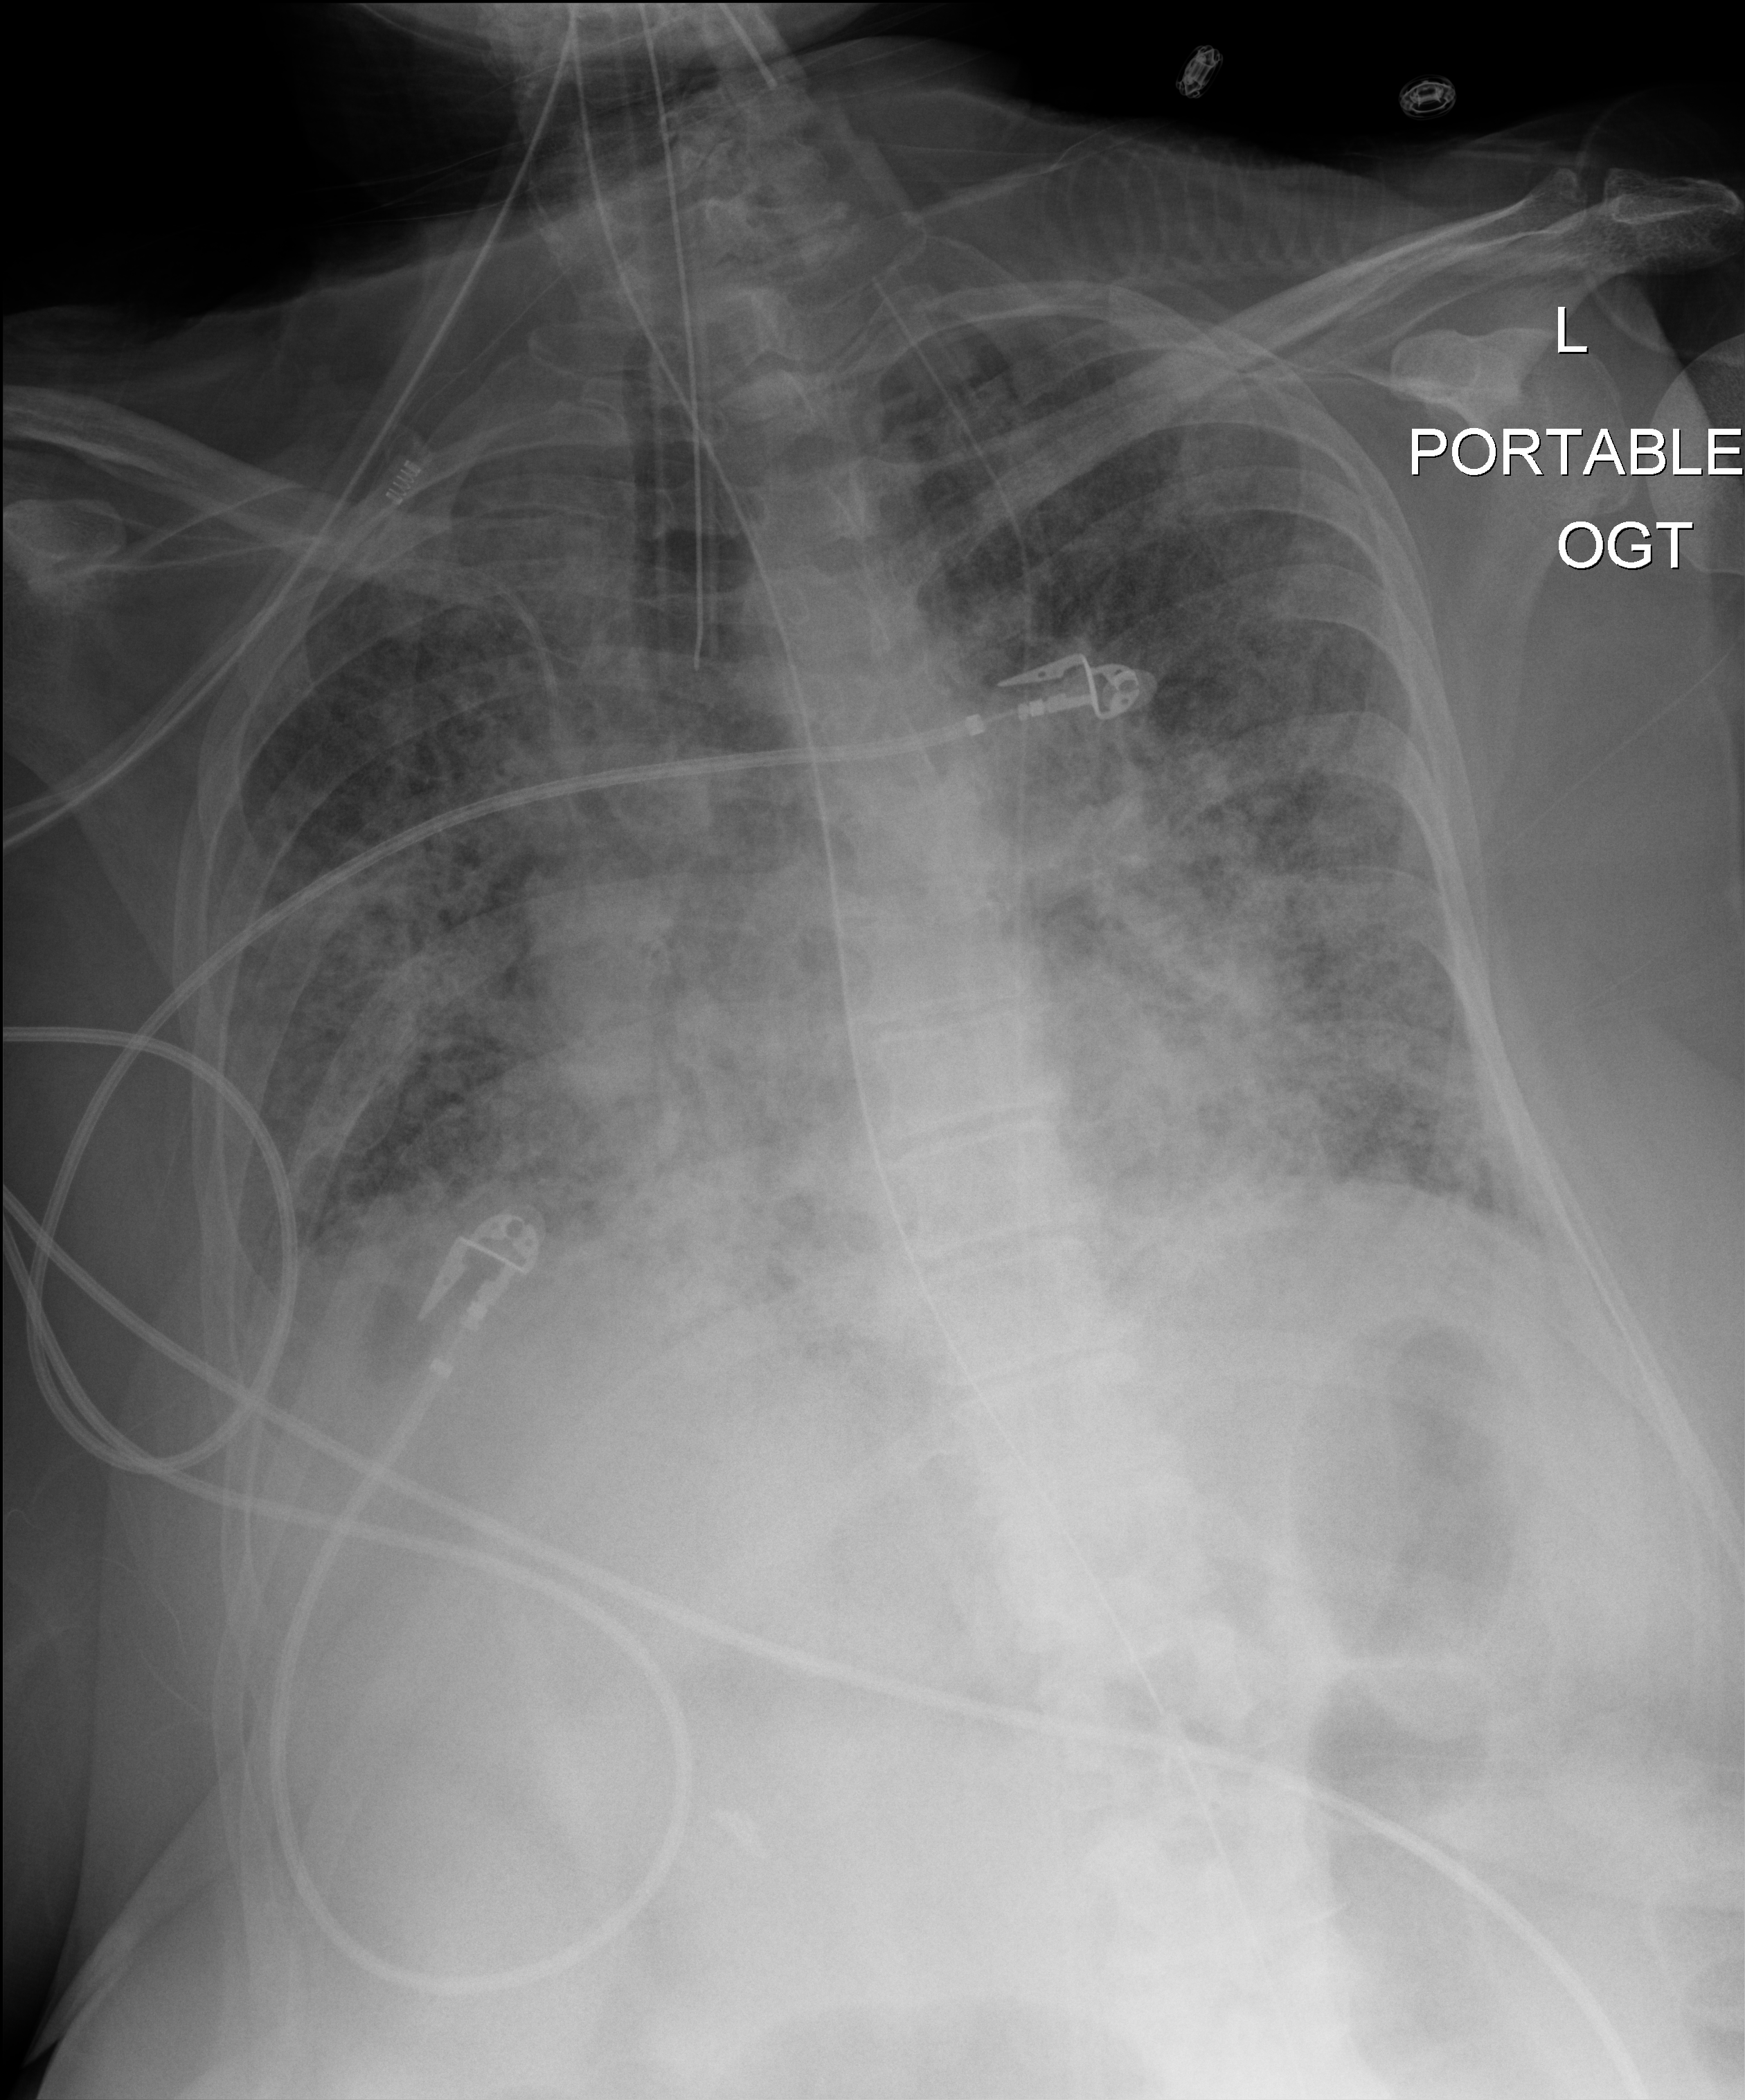
Chest X-ray (portable); anteroposterior (AP) projection. Patient hospitalised with COVID-19; female, aged 60–74 years.
Hospital-stay facts (about this admission, not read from this image; timing relative to this image not recorded): admitted to intensive care during this hospital stay: yes.